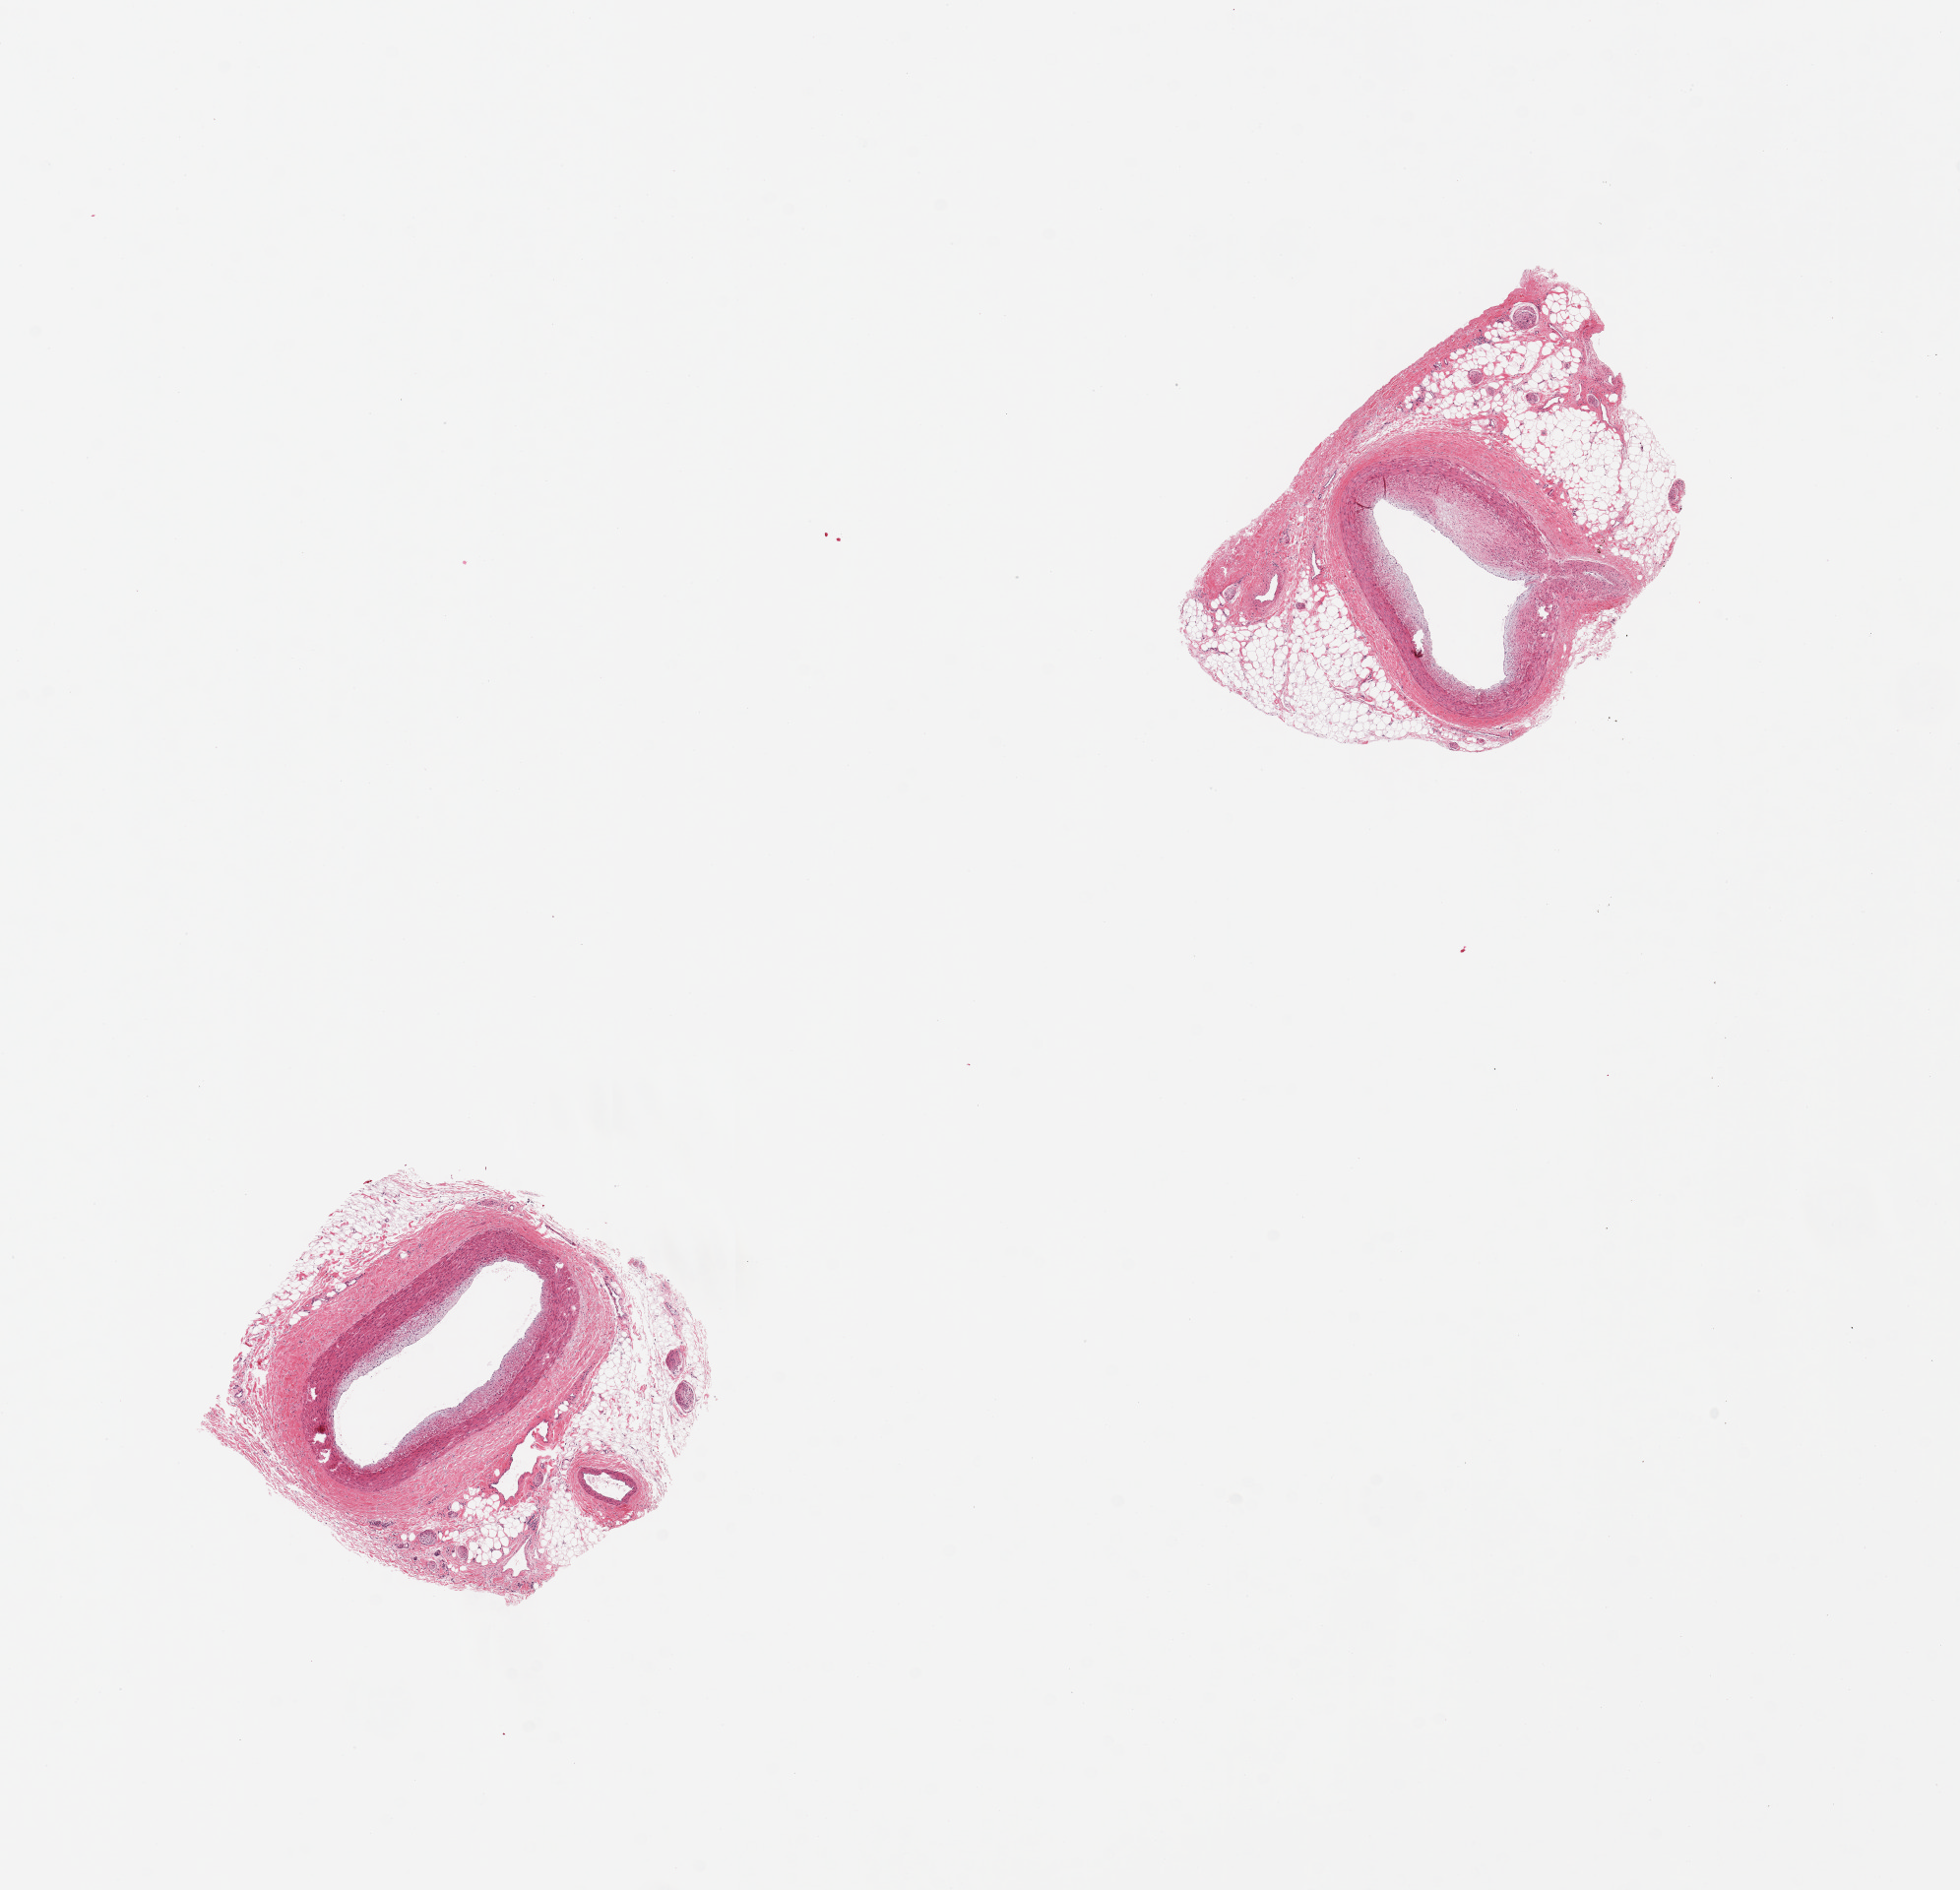
Whole-slide image, haematoxylin and eosin stain — low-resolution overview of the scanned area, about 15.8 x 15.2 mm. PAXgene-fixed paraffin-embedded (PFPE) section. Sampled site (target tissue): coronary artery. Tissue donor sample. Donor: male.
Reviewer comment on this tissue sample: 2 pieces, both with rims of 1-2mm adherent fat, early luminal atherotic deposits noted ~0.1-0.2mm.